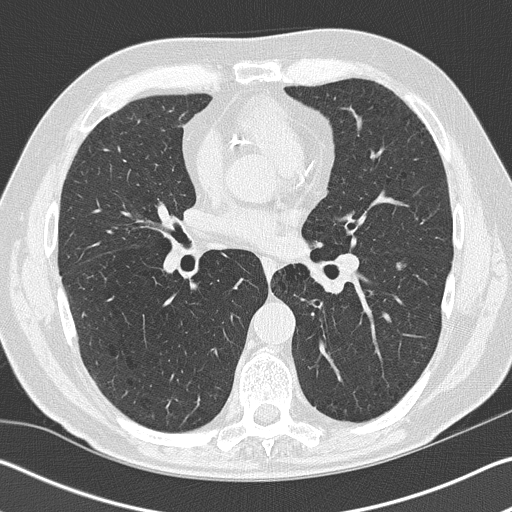
Low-dose screening chest CT, axial slice. Baseline screening round. Lung window (W 1500 / L -600 HU). 2 mm slice thickness. Lung (sharp) reconstruction kernel (B50f). 120 kVp. 512 × 512 image matrix, field of view 340 × 340 mm. Male, age 65 years at enrolment. Current smoker at enrolment.
Lesion marked by an expert reader, bounding box (x1, y1, x2, y2) in pixels: (376, 248, 423, 285). No non-calcified nodule or mass ≥4 mm was recorded by the screening reader at this exam. Official screen result: negative screen, minor abnormalities not suspicious for lung cancer. Later outcome: lung cancer diagnosed 460 days after this screen (after the second annual screen) — non-small cell carcinoma, left lower lobe, right hilum, poorly differentiated (G3), stage IV (AJCC 6th edition), 5 mm at pathology.